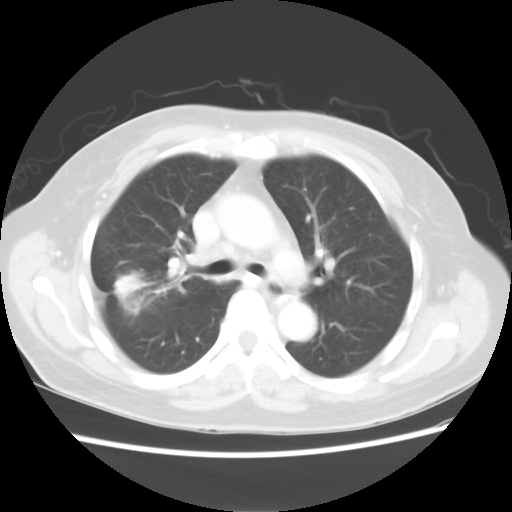
Chest CT, one axial slice. Slice 47 of 80 in the series (ordered by position). Lung window (W 1500 / L -600 HU). 512 × 512 image matrix, field of view 342 × 342 mm. Patient: female, 67 years. From the clinical record (not read from this slice): clinical TNM (as recorded): T1c N1 M0.
Outlined on this slice (bounding box drawn by a radiologist):
- lung tumour (recorded histology: adenocarcinoma): box from (x=114, y=268) to (x=158, y=326) px